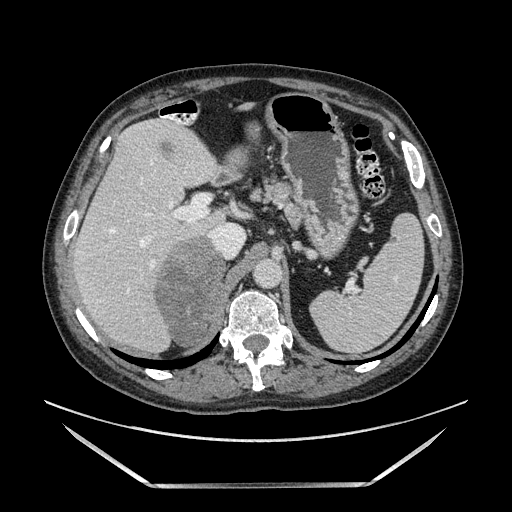
Contrast-enhanced abdominal CT, one axial slice; slice 99 of 185 in the series (ordered by position); soft-tissue window (W 400 / L 40 HU); 1.25 mm slice thickness; 512 × 512 image matrix, field of view 440 × 440 mm. Male patient. Case-level facts recorded for this patient, not image findings: diagnosis: adrenocortical carcinoma; tumour side: right adrenal; tumour size at pathology: 10.3 cm; Ki-67 index: 20 %; stage (as recorded): 3.
Outlined on this slice (semi-automatic segmentation, software-assisted and operator-edited):
- mass: bounding box (x1, y1, x2, y2) in pixels: (158, 236, 227, 345)